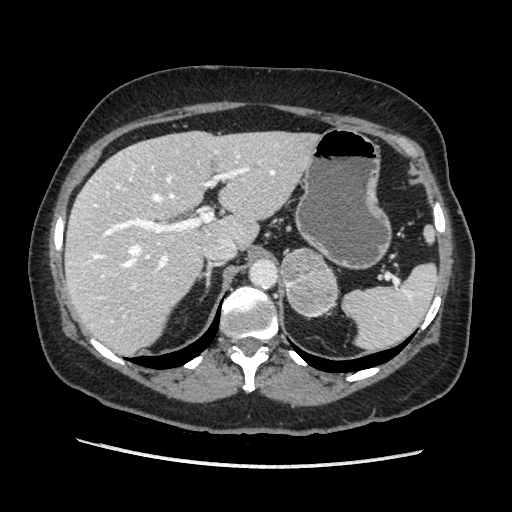
Contrast-enhanced abdominal CT, one axial slice; position 135 of 203 along the scan axis; soft-tissue window (W 400 / L 40 HU); 1.25 mm slice thickness; 512 × 512 image matrix. Female patient. Case-level facts recorded for this patient, not image findings: diagnosis: adrenocortical carcinoma; tumour side: left adrenal; tumour size at pathology: 6.5 cm; Ki-67 index: 22 %; stage (as recorded): 2.
Annotated regions visible in this slice (semi-automatically segmented with operator editing):
- mass: bounding box <282,248,338,315> (left, top, right, bottom; pixels)